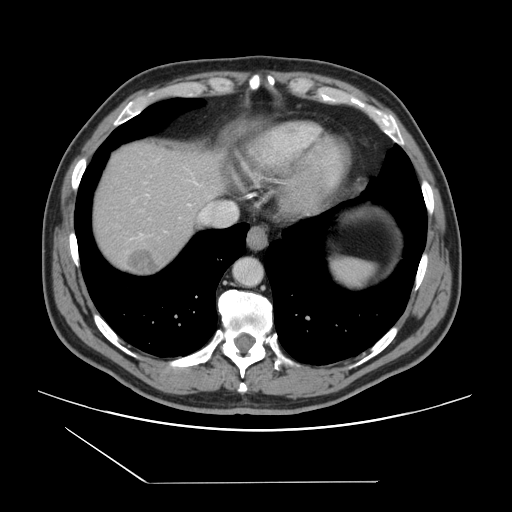
Contrast-enhanced abdominal CT, one axial slice; position 130 of 157 along the scan axis; intravenous contrast given; soft-tissue window (W 400 / L 40 HU); 2.5 mm slice thickness; 512 × 512 image matrix, field of view 407 × 407 mm. Male patient, age 61 years. Case-level facts recorded for this patient, not image findings: diagnosis: colorectal cancer liver metastases, imaged before liver resection.
Structures marked on this image (outlined manually by an expert reader):
- hepatic veins: bounding box [x1, y1, x2, y2] px = [188, 203, 237, 222]
- liver: [91, 142, 222, 276]
- planned liver remnant (the part of the liver to remain after resection): [92, 141, 222, 232]
- liver metastasis: [127, 248, 159, 273]